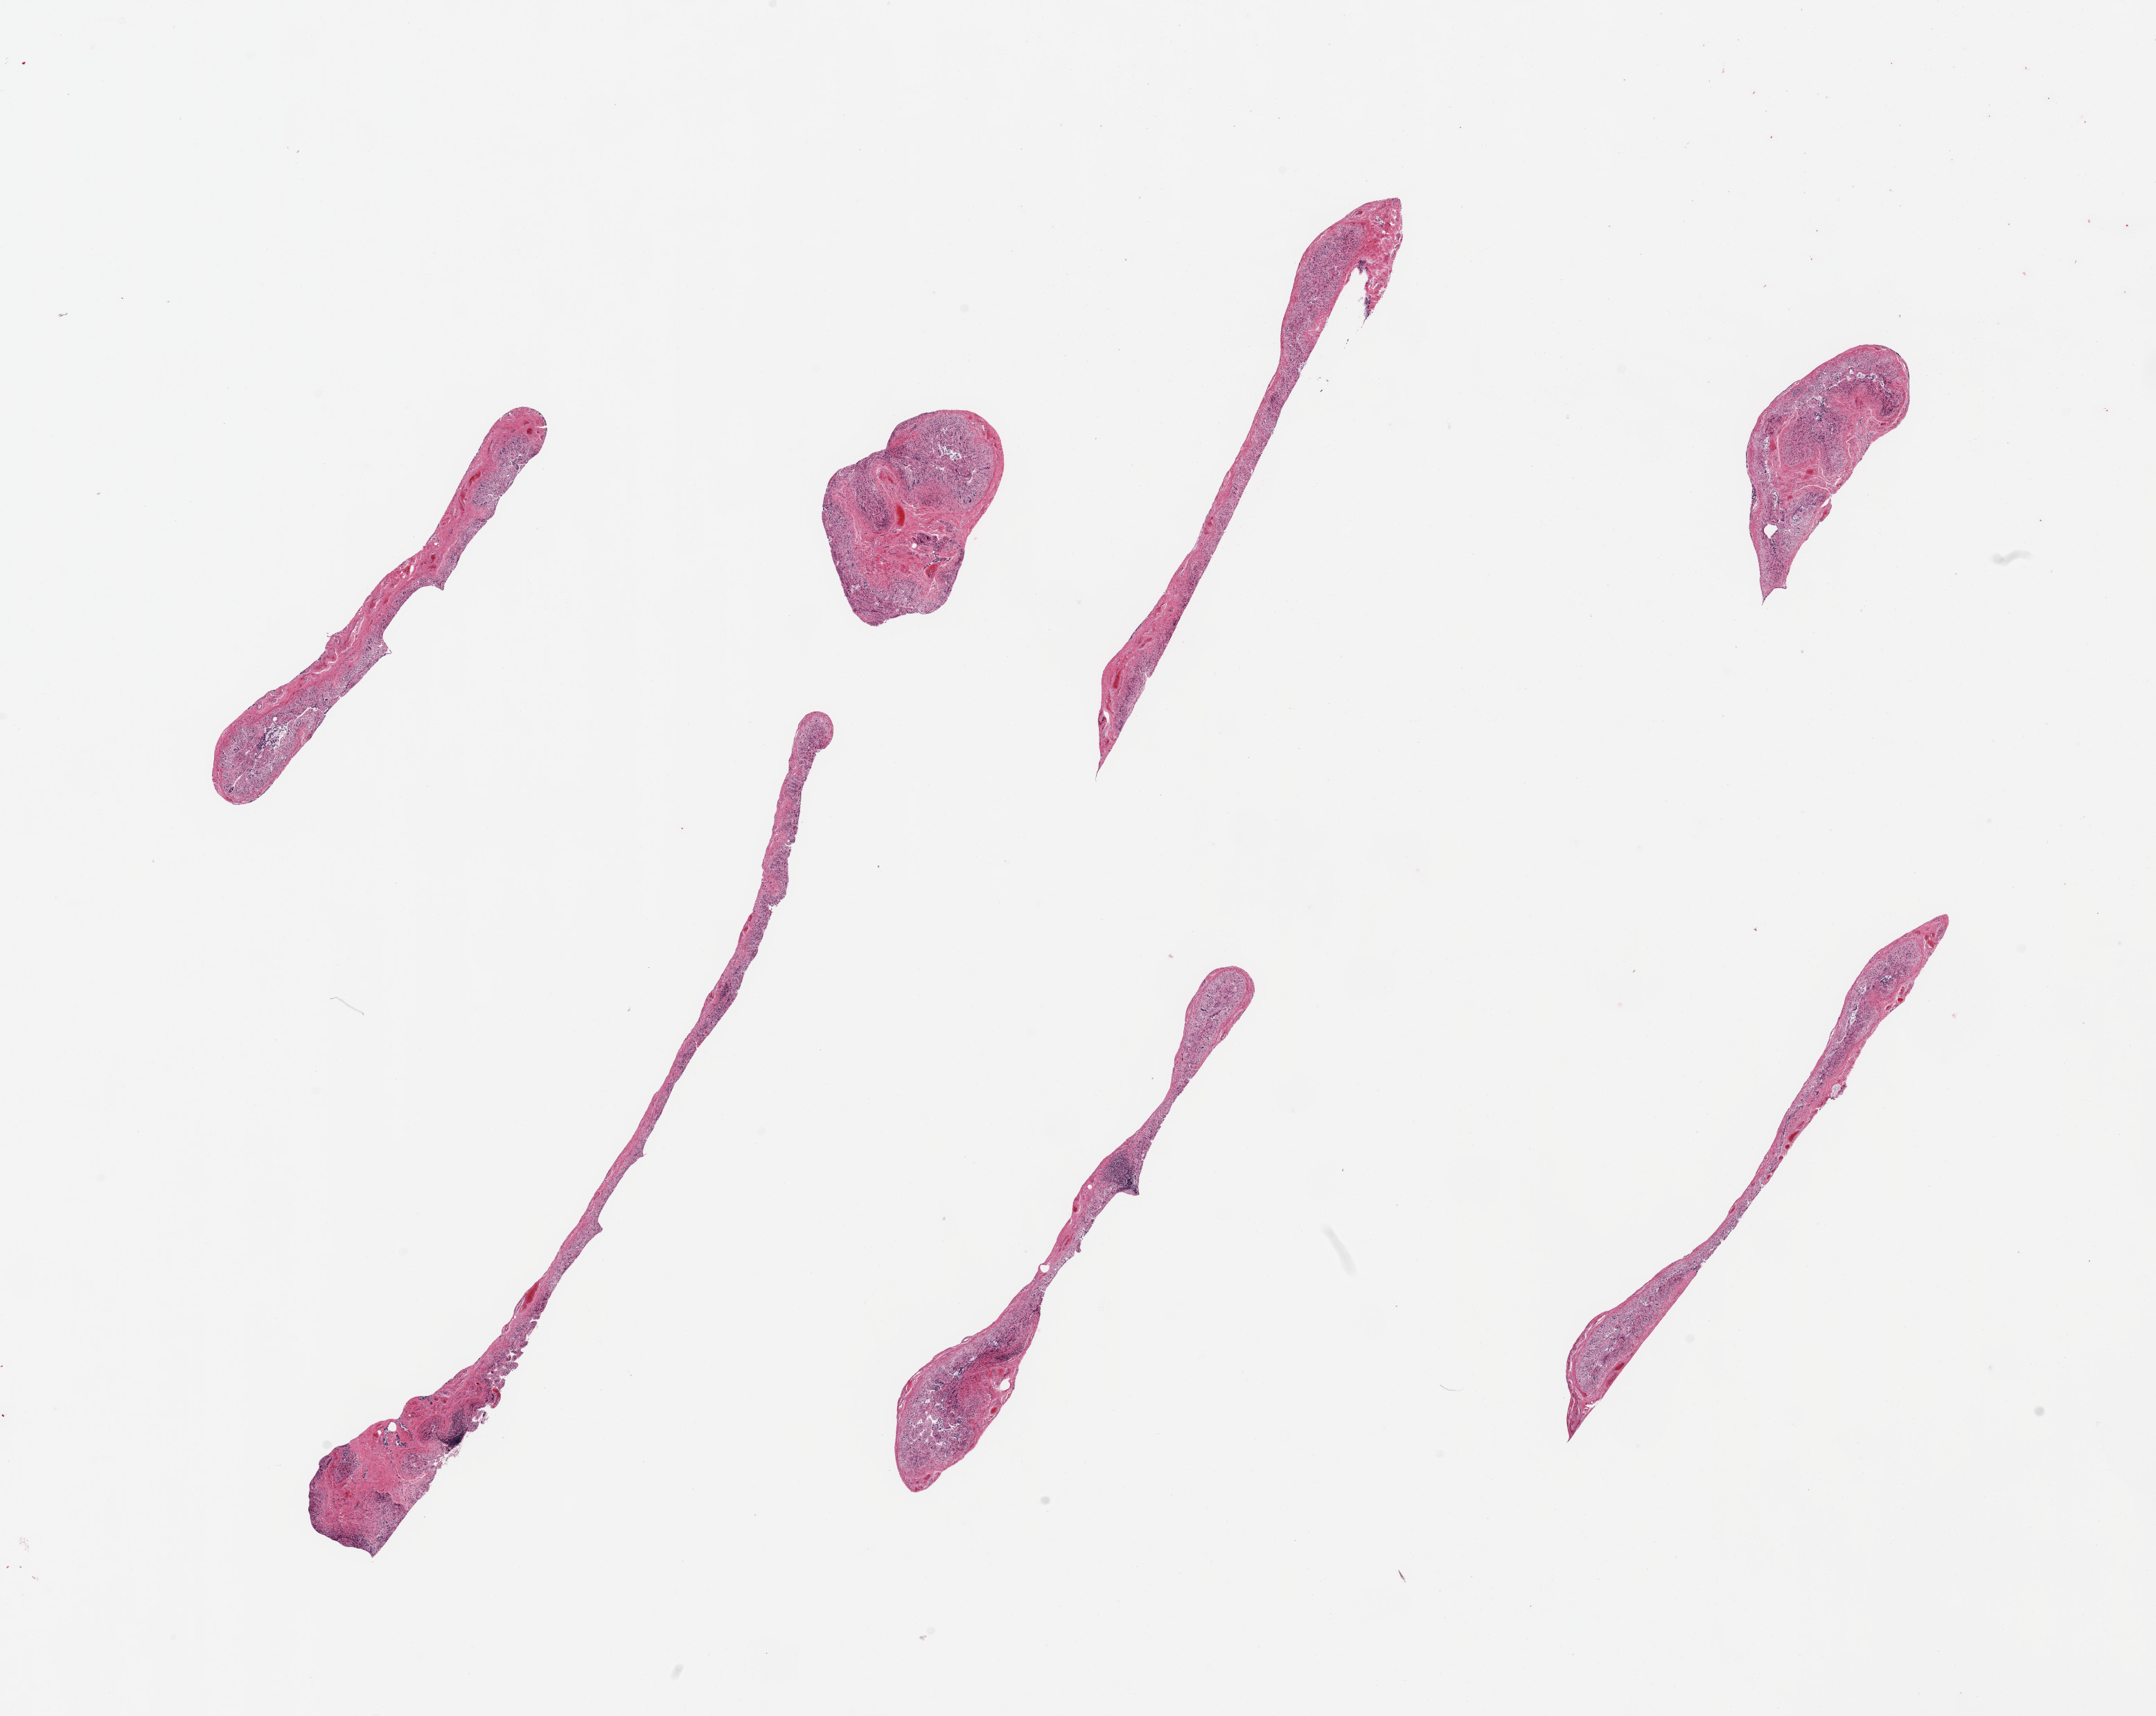
Whole-slide image, H&E stain, brightfield, low-resolution overview of the scanned area, about 24.6 x 19.6 mm (from a 20x scan); PAXgene-fixed paraffin-embedded (PFPE) section; target tissue: ileum; tissue donor sample. Donor: male.
Pathologist's review note for this sample: 6 pieces; autolyzed mucosa and too few lymphoid aggregates to warrant analysis(<5%).